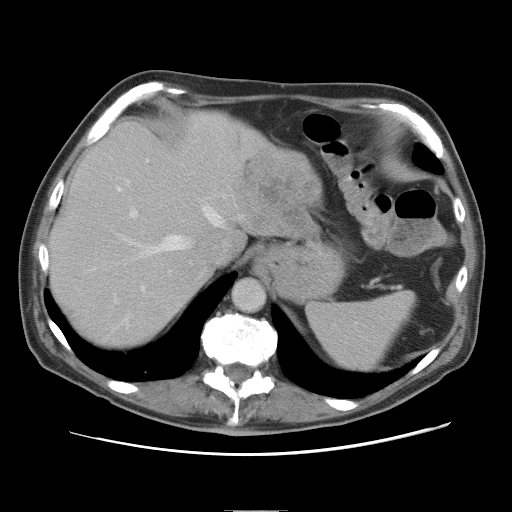
Contrast-enhanced abdominal CT, one axial slice. Slice 62 of 89 in the series (ordered by position). Intravenous contrast given. Soft-tissue window (W 400 / L 40 HU). 5 mm slice thickness. 512 × 512 image matrix, field of view 375 × 375 mm. Male patient, age 69 years. Case-level facts recorded for this patient, not image findings: diagnosis: colorectal cancer liver metastases, imaged before liver resection; multiple liver metastases: no; largest metastasis: 8.5 cm; disease in both lobes: no.
Structures marked on this image (manually delineated by an expert):
- hepatic veins: bounding box <116,186,225,290> (left, top, right, bottom; pixels)
- liver: <51,112,317,346>
- planned liver remnant (the part of the liver to remain after resection): <51,112,246,346>
- portal vein (with intrahepatic branches): <128,159,148,218>
- liver metastasis: <242,153,317,234>